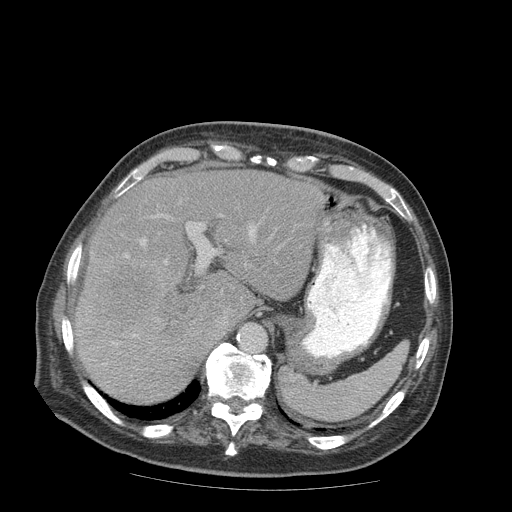
Contrast-enhanced abdominal CT (liver protocol), one axial slice; position 63 of 99 along the scan axis; reconstruction kernel STANDARD; 140 kVp; soft-tissue window (W 400 / L 40 HU); 2.5 mm slice thickness; 512 × 512 image matrix, field of view 420 × 420 mm. From the clinical record (not read from this slice): diagnosis: hepatocellular carcinoma (patient treated with transarterial chemoembolisation; whether this scan precedes or follows treatment is not stated here); TNM stage (as recorded): Stage-IIIB; Child-Pugh class: A.
Outlined on this slice (semi-automatically segmented with operator editing):
- liver parenchyma outside the tumour (the mass and vessels are separate outlines, so this box may not span the whole liver): bounding box <74,170,324,402> (left, top, right, bottom; pixels)
- mass: <95,261,160,329>
- liver vessels: <111,227,255,344>